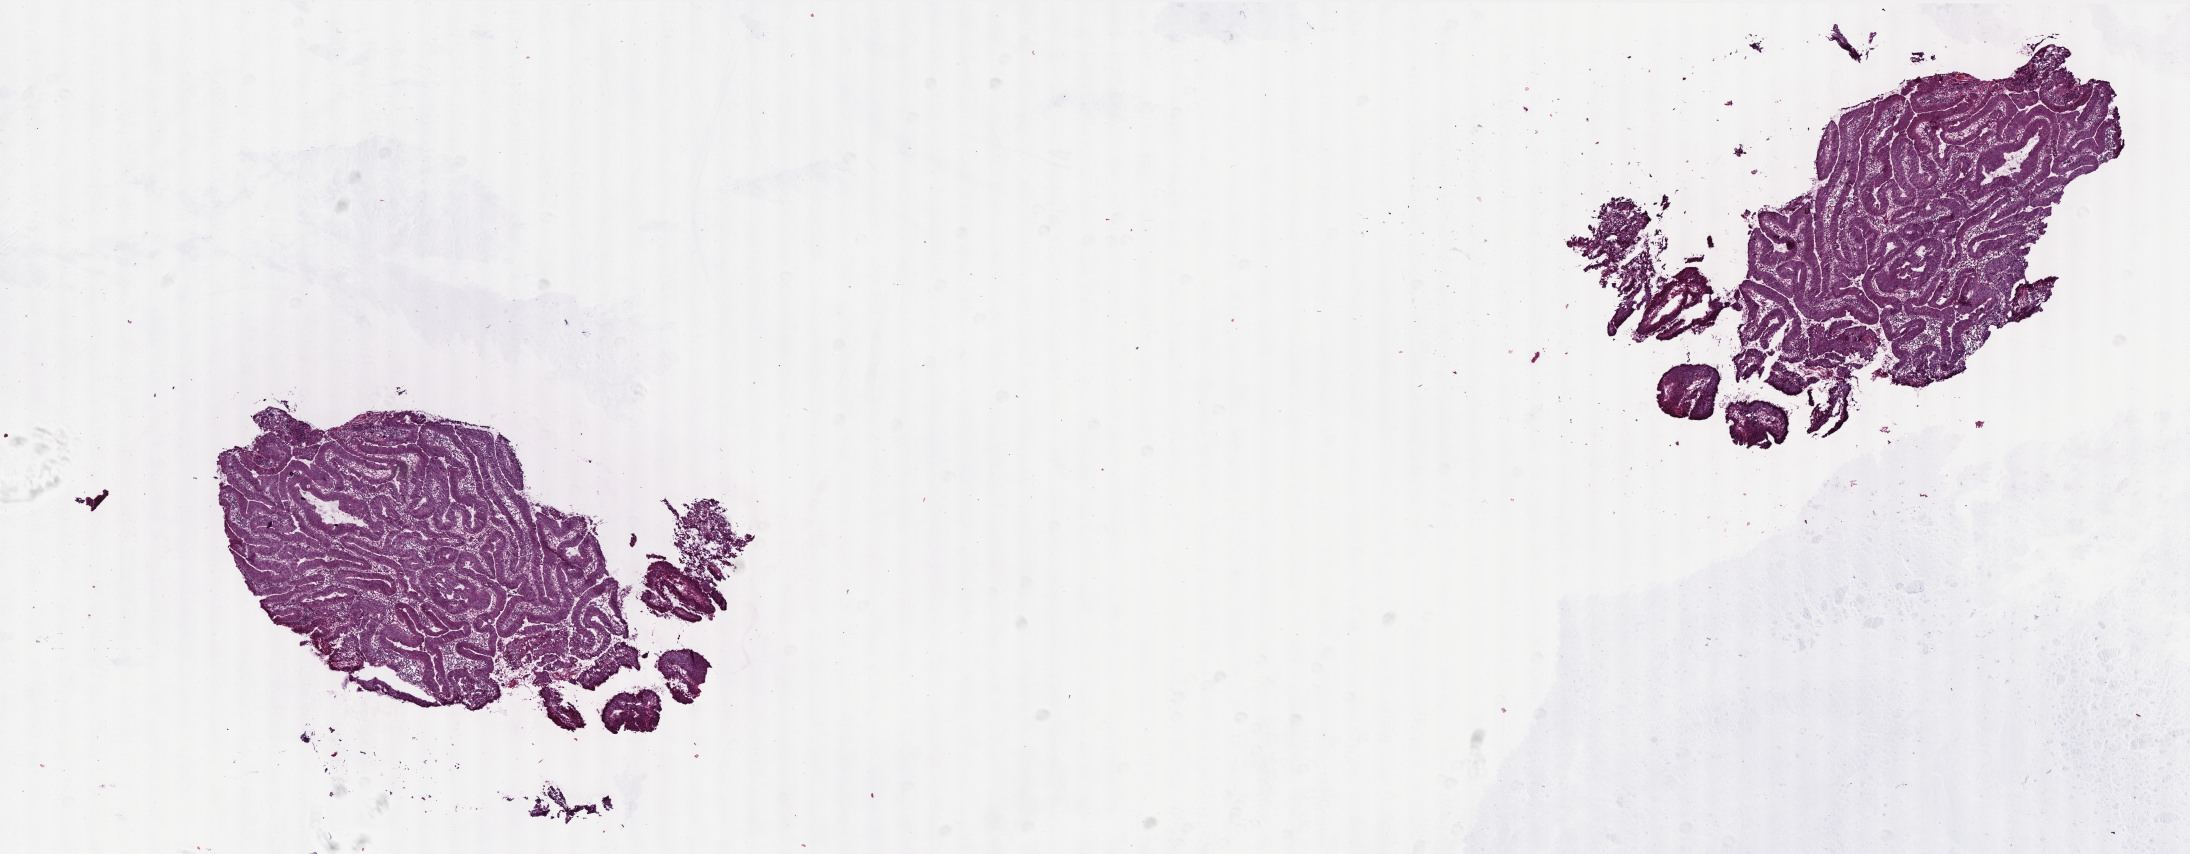
Whole-slide histology image, H&E-stained, a low-resolution overview of the entire scanned area, about 17.6 x 6.8 mm. Frozen section. Sample: primary tumour, colon. Male, age 80 years at initial diagnosis. Pathologist review of this section (percent, as recorded): tumour cells 95%, tumour nuclei 80%, normal cells 0%, stromal cells 4%, necrosis 1%. Infiltration values recorded for this section: lymphocyte infiltration 8%, monocyte infiltration 4%, neutrophil infiltration 2%.
Diagnosis: Adenocarcinoma, NOS (sigmoid colon). Lymph nodes positive (case pathology): 0 of 17 examined. AJCC pathologic stage: I (6th edition).